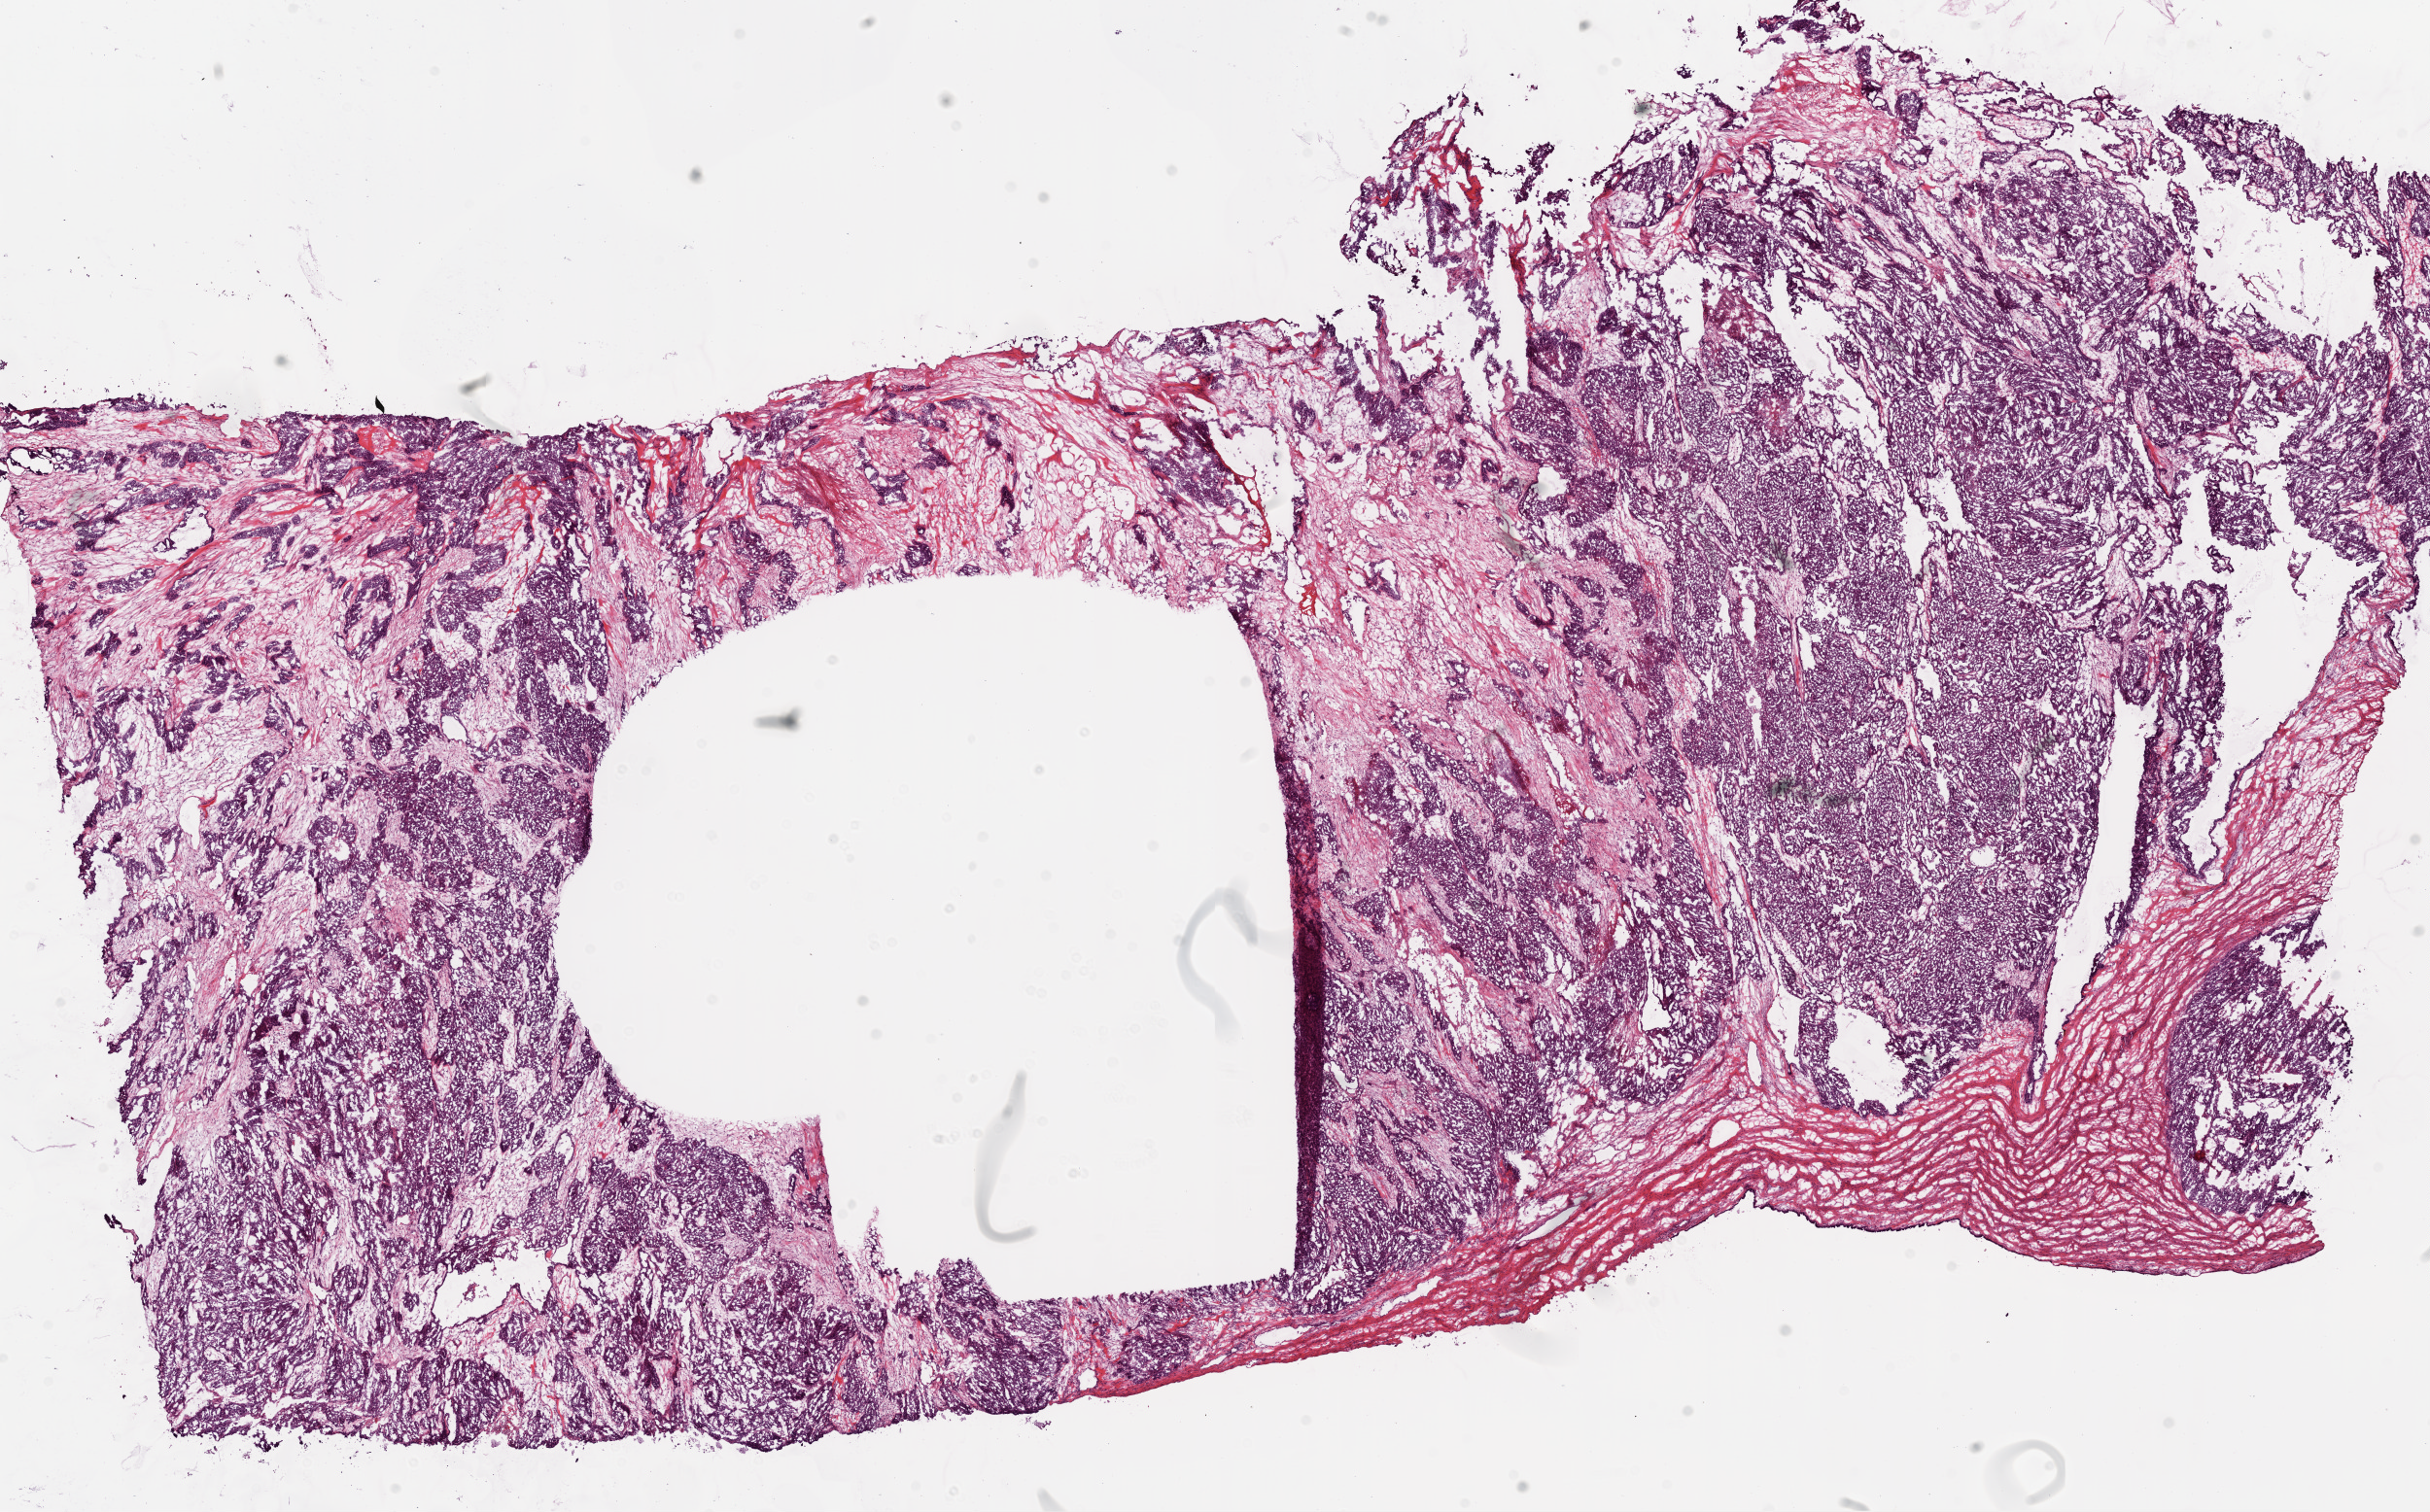
H&E whole-slide image — whole scanned area (about 20.1 x 12.5 mm) shown as a low-resolution overview; frozen section; sample: primary tumour, ovary. Female patient; age at initial diagnosis 55 years. Slide review estimates, as recorded: tumour cells 94%, tumour nuclei 95%.
Pathologic diagnosis: Serous cystadenocarcinoma, NOS.